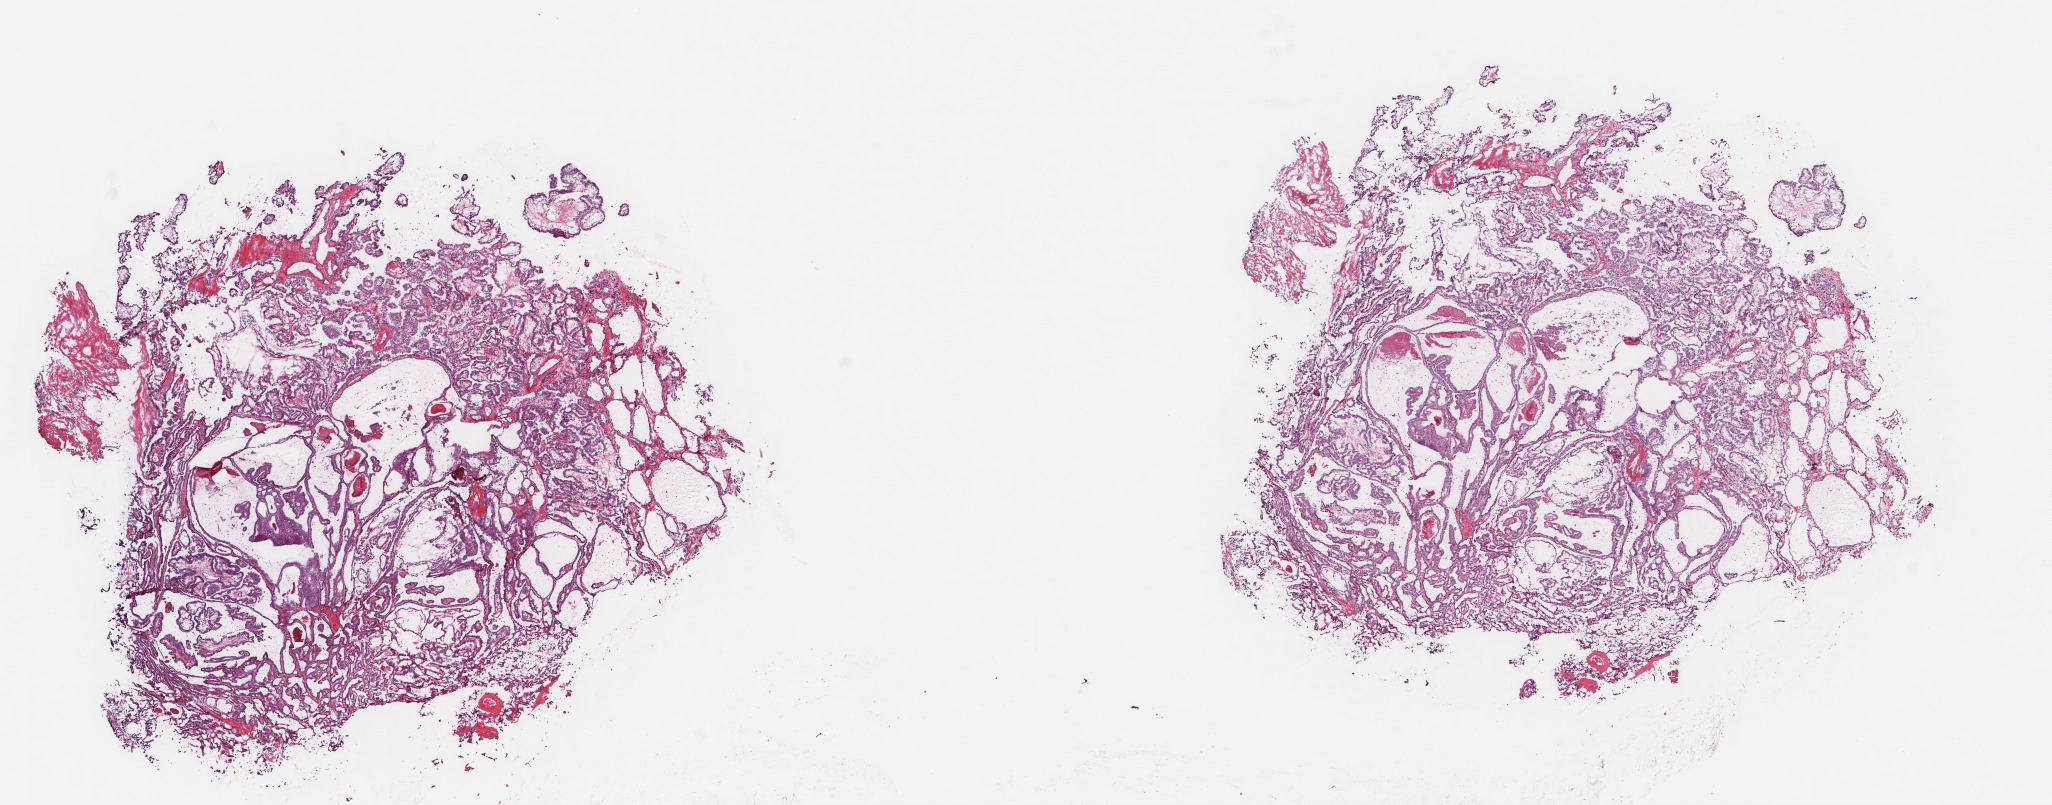
H&E-stained whole-slide image — a low-resolution overview of the entire scanned area, about 16.3 x 6.4 mm (slide scanned at 40x). Frozen section from the top of the tissue portion. Thyroid, primary tumour sample. Patient: male, age at initial diagnosis 33 years. Composition of this section per pathologist review: tumour cells 85%, tumour nuclei 85%, normal cells 0%, stromal cells 15%, necrosis 0%. Inflammatory infiltration, as recorded: lymphocyte infiltration 0%, monocyte infiltration 0%, neutrophil infiltration 0%.
- histologic diagnosis: Papillary adenocarcinoma, NOS (thyroid gland)
- AJCC pathologic stage: I (7th edition)